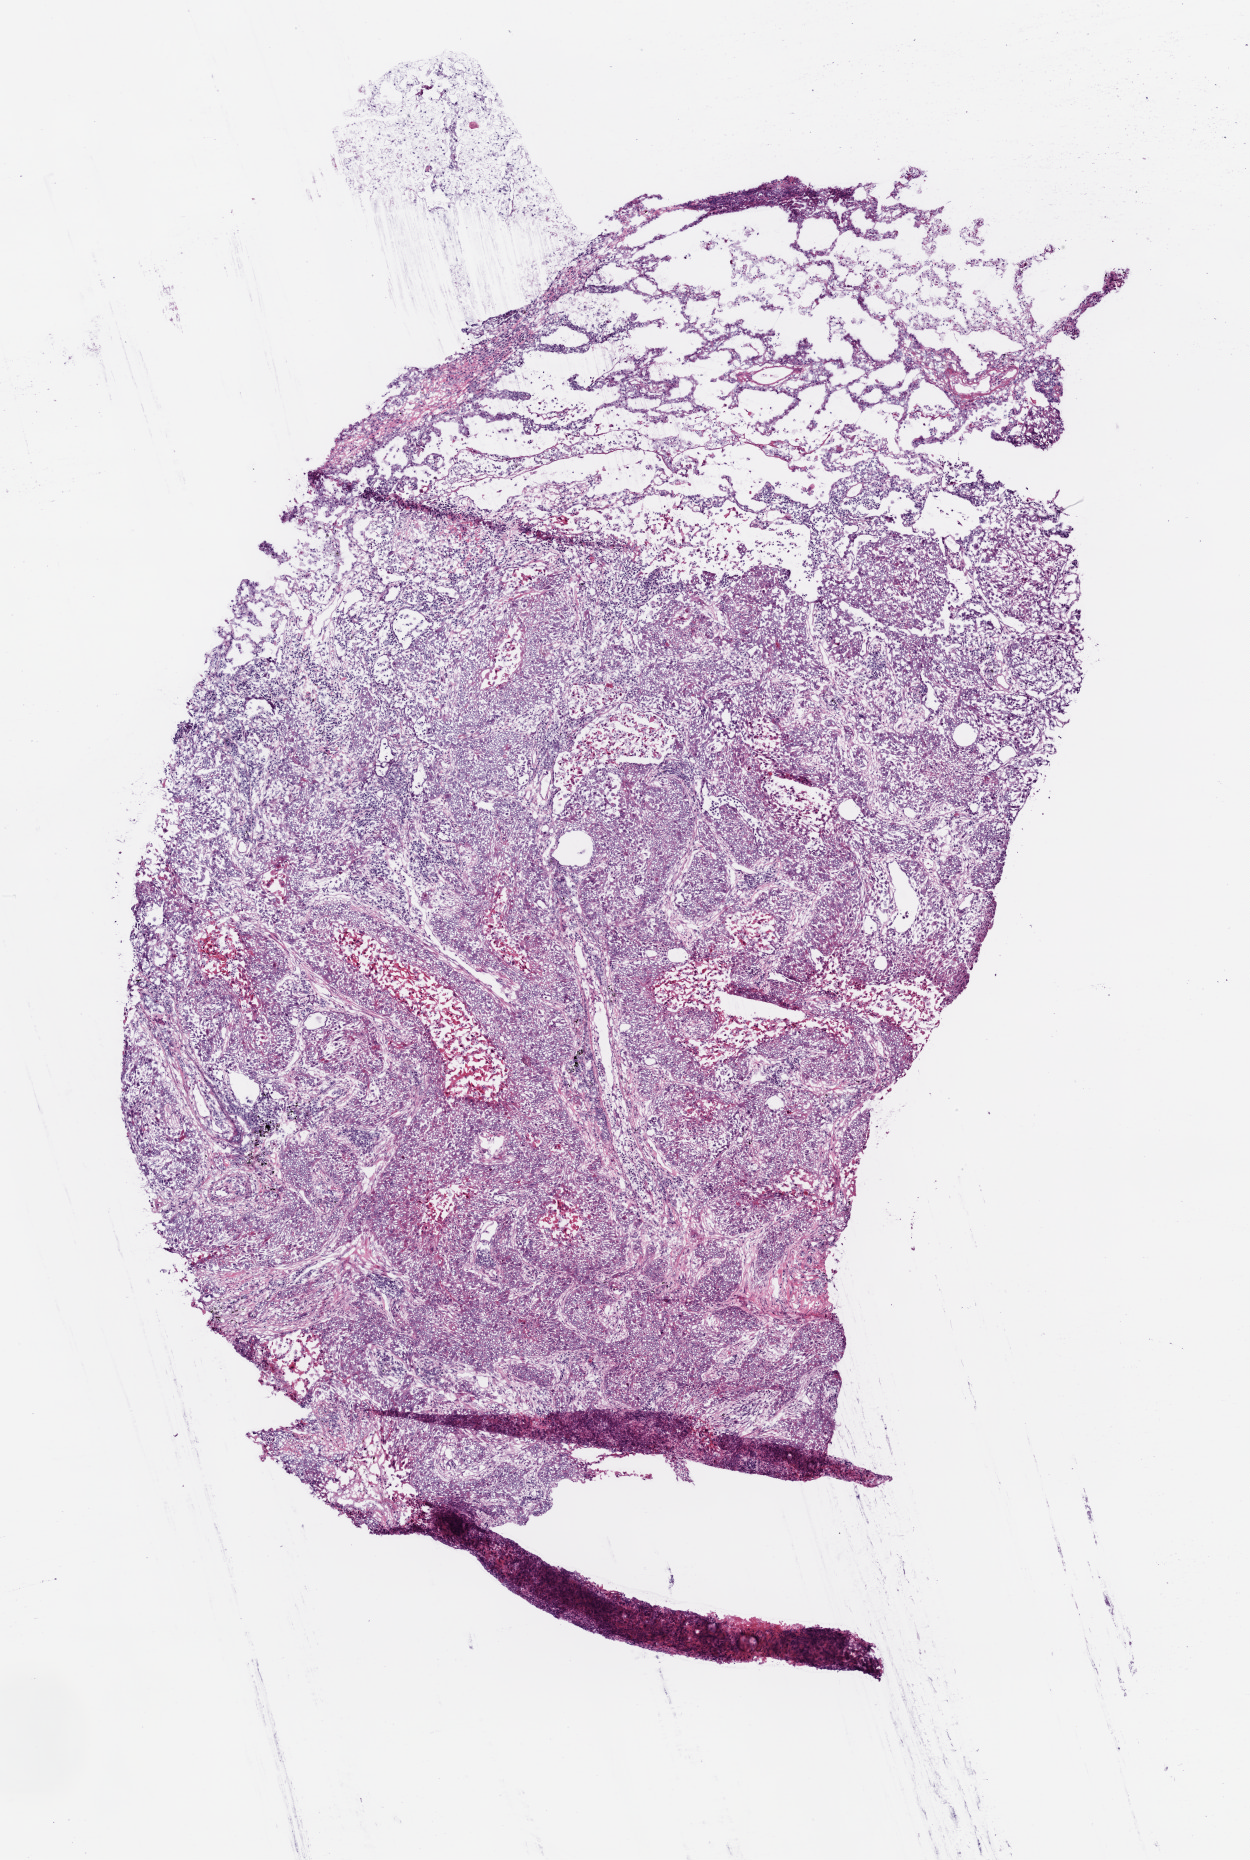
Whole-slide histology image, H&E-stained — a low-resolution overview of the entire scanned area, about 5.0 x 7.5 mm (from a 20x scan). Frozen section. Sample: primary tumour, lung. Female patient; age at initial diagnosis 73 years. Composition of this section per pathologist review: tumour cells 50%, tumour nuclei 75%, normal cells 30%, stromal cells 5%, necrosis 15%.
AJCC pathologic stage: IB (6th edition). Histologic diagnosis: Squamous cell carcinoma, NOS (upper lobe, lung).